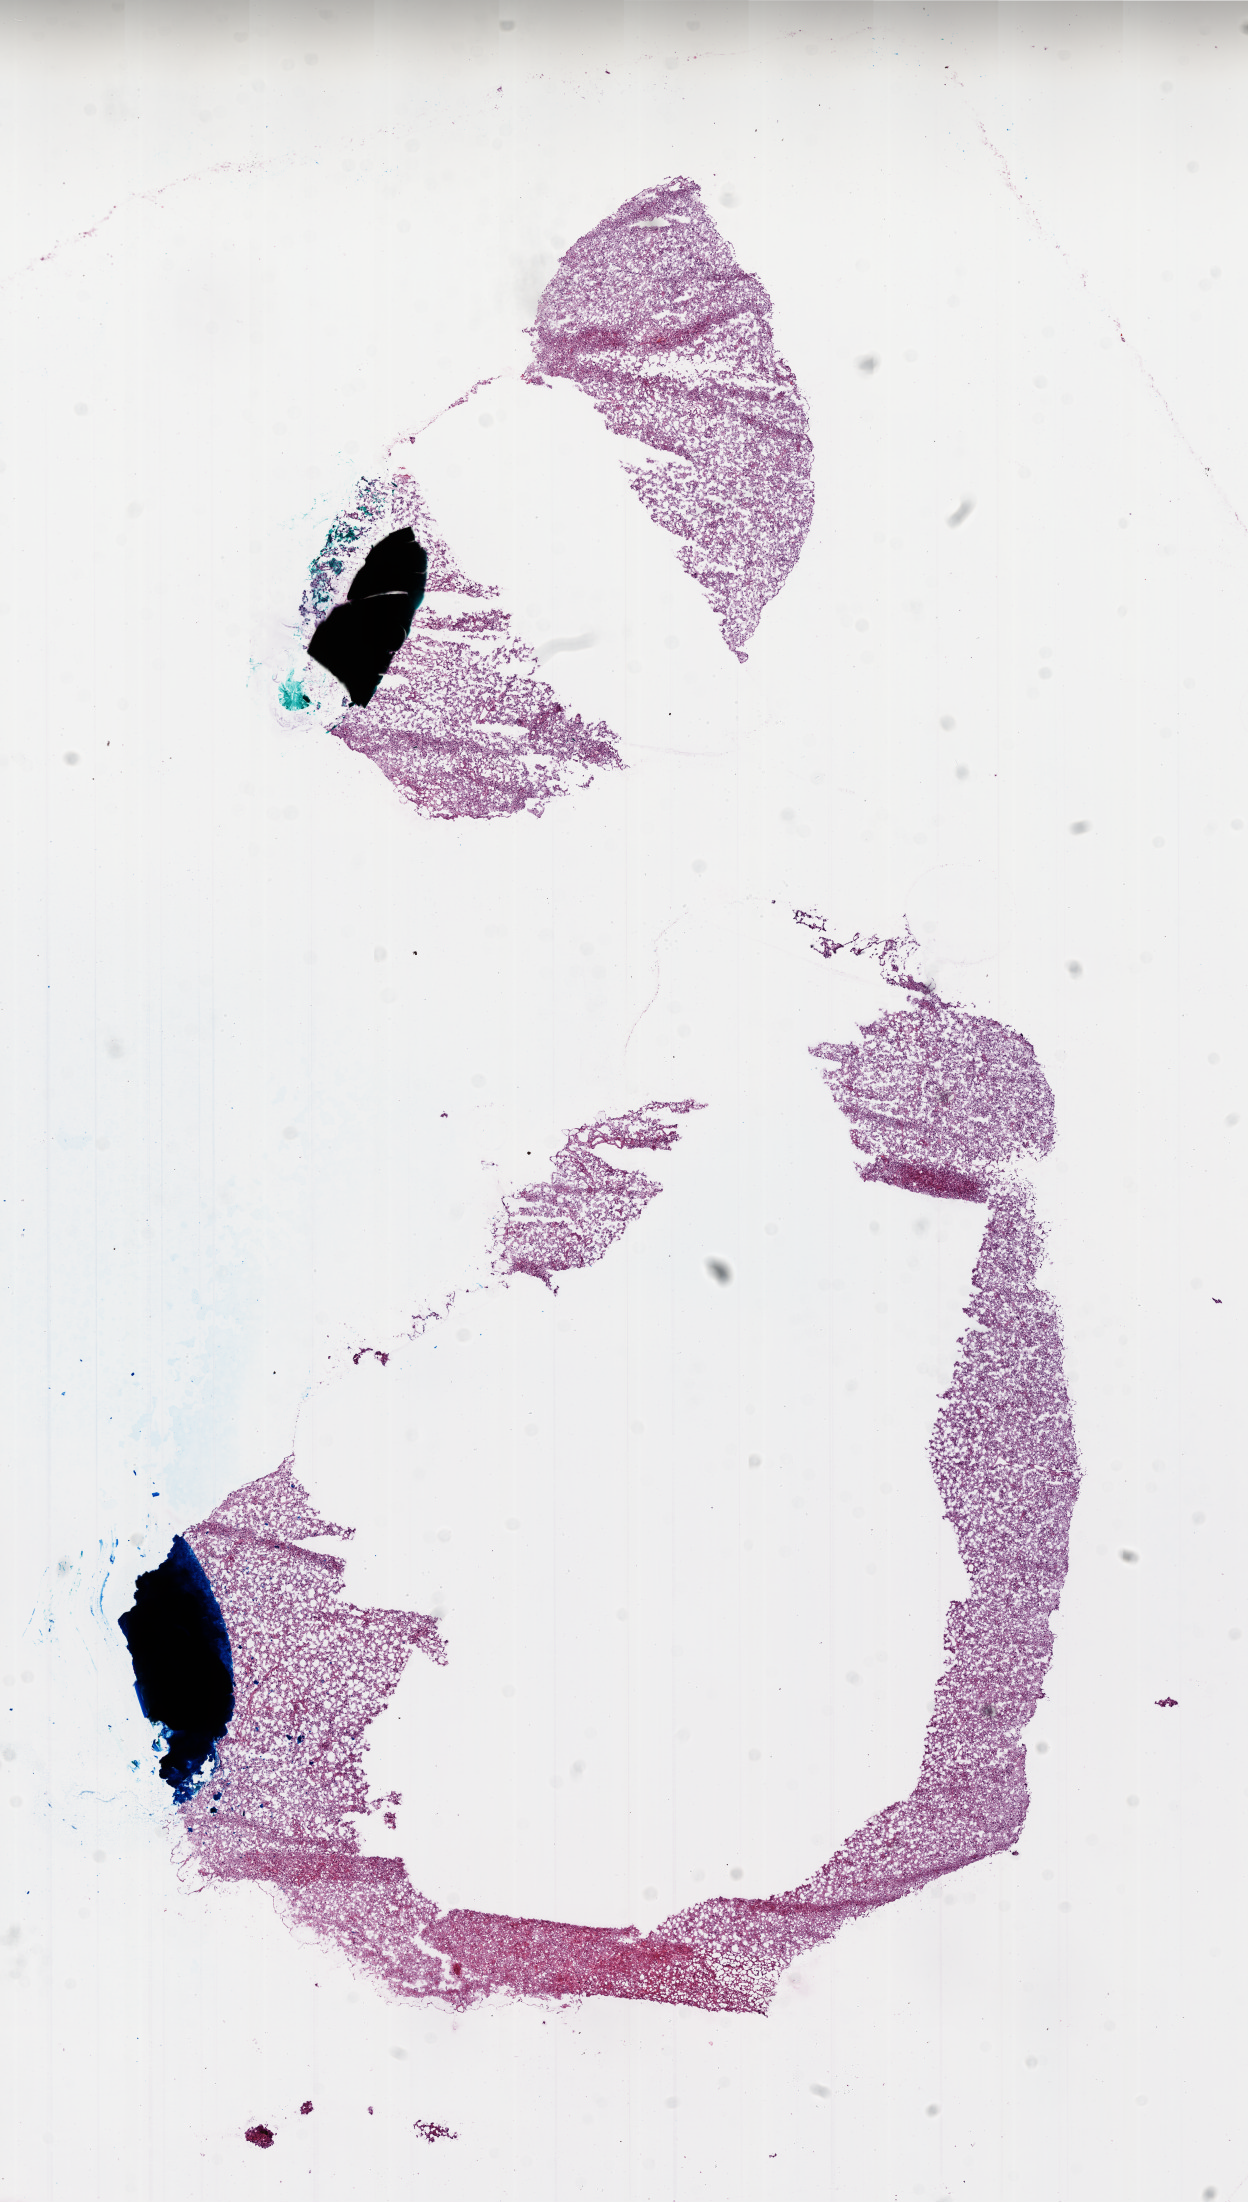
Digitized Hematoxylin and eosin (H&E) stained tissue section (whole slide) — whole scanned area (about 10.0 x 17.6 mm, slide scanned at 20x) shown as a low-resolution overview, frozen section, primary tumour sample from the brain. Patient: male, age at initial diagnosis 67 years. Slide review estimates, as recorded: tumour cells 100%, tumour nuclei 100%, normal cells 0%, stromal cells 0%, necrosis 0%. Infiltration values recorded for this section: lymphocyte infiltration 0%.
Histologic diagnosis: Glioblastoma.